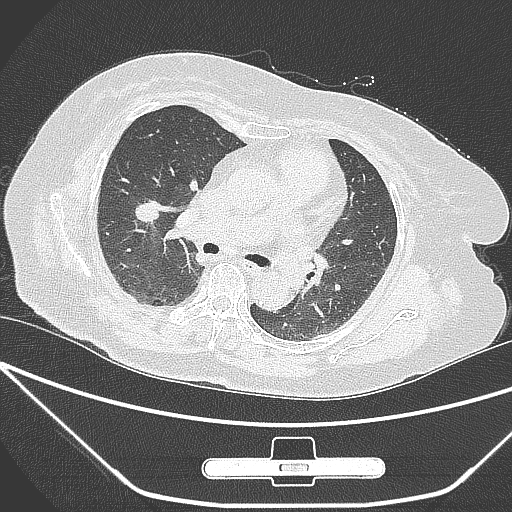
Chest CT, one axial slice; position 158 of 245 along the scan axis; 120 kVp; lung window (W 1500 / L -600 HU); 1 mm slice thickness; 512 × 512 image matrix. Female patient, age 65 years. From the clinical record (not read from this slice): clinical TNM (as recorded): T1c N0 M0.
Annotated regions visible in this slice (bounding box drawn by a radiologist):
- lung tumour (recorded histology: adenocarcinoma): box from (x=119, y=185) to (x=160, y=236) px